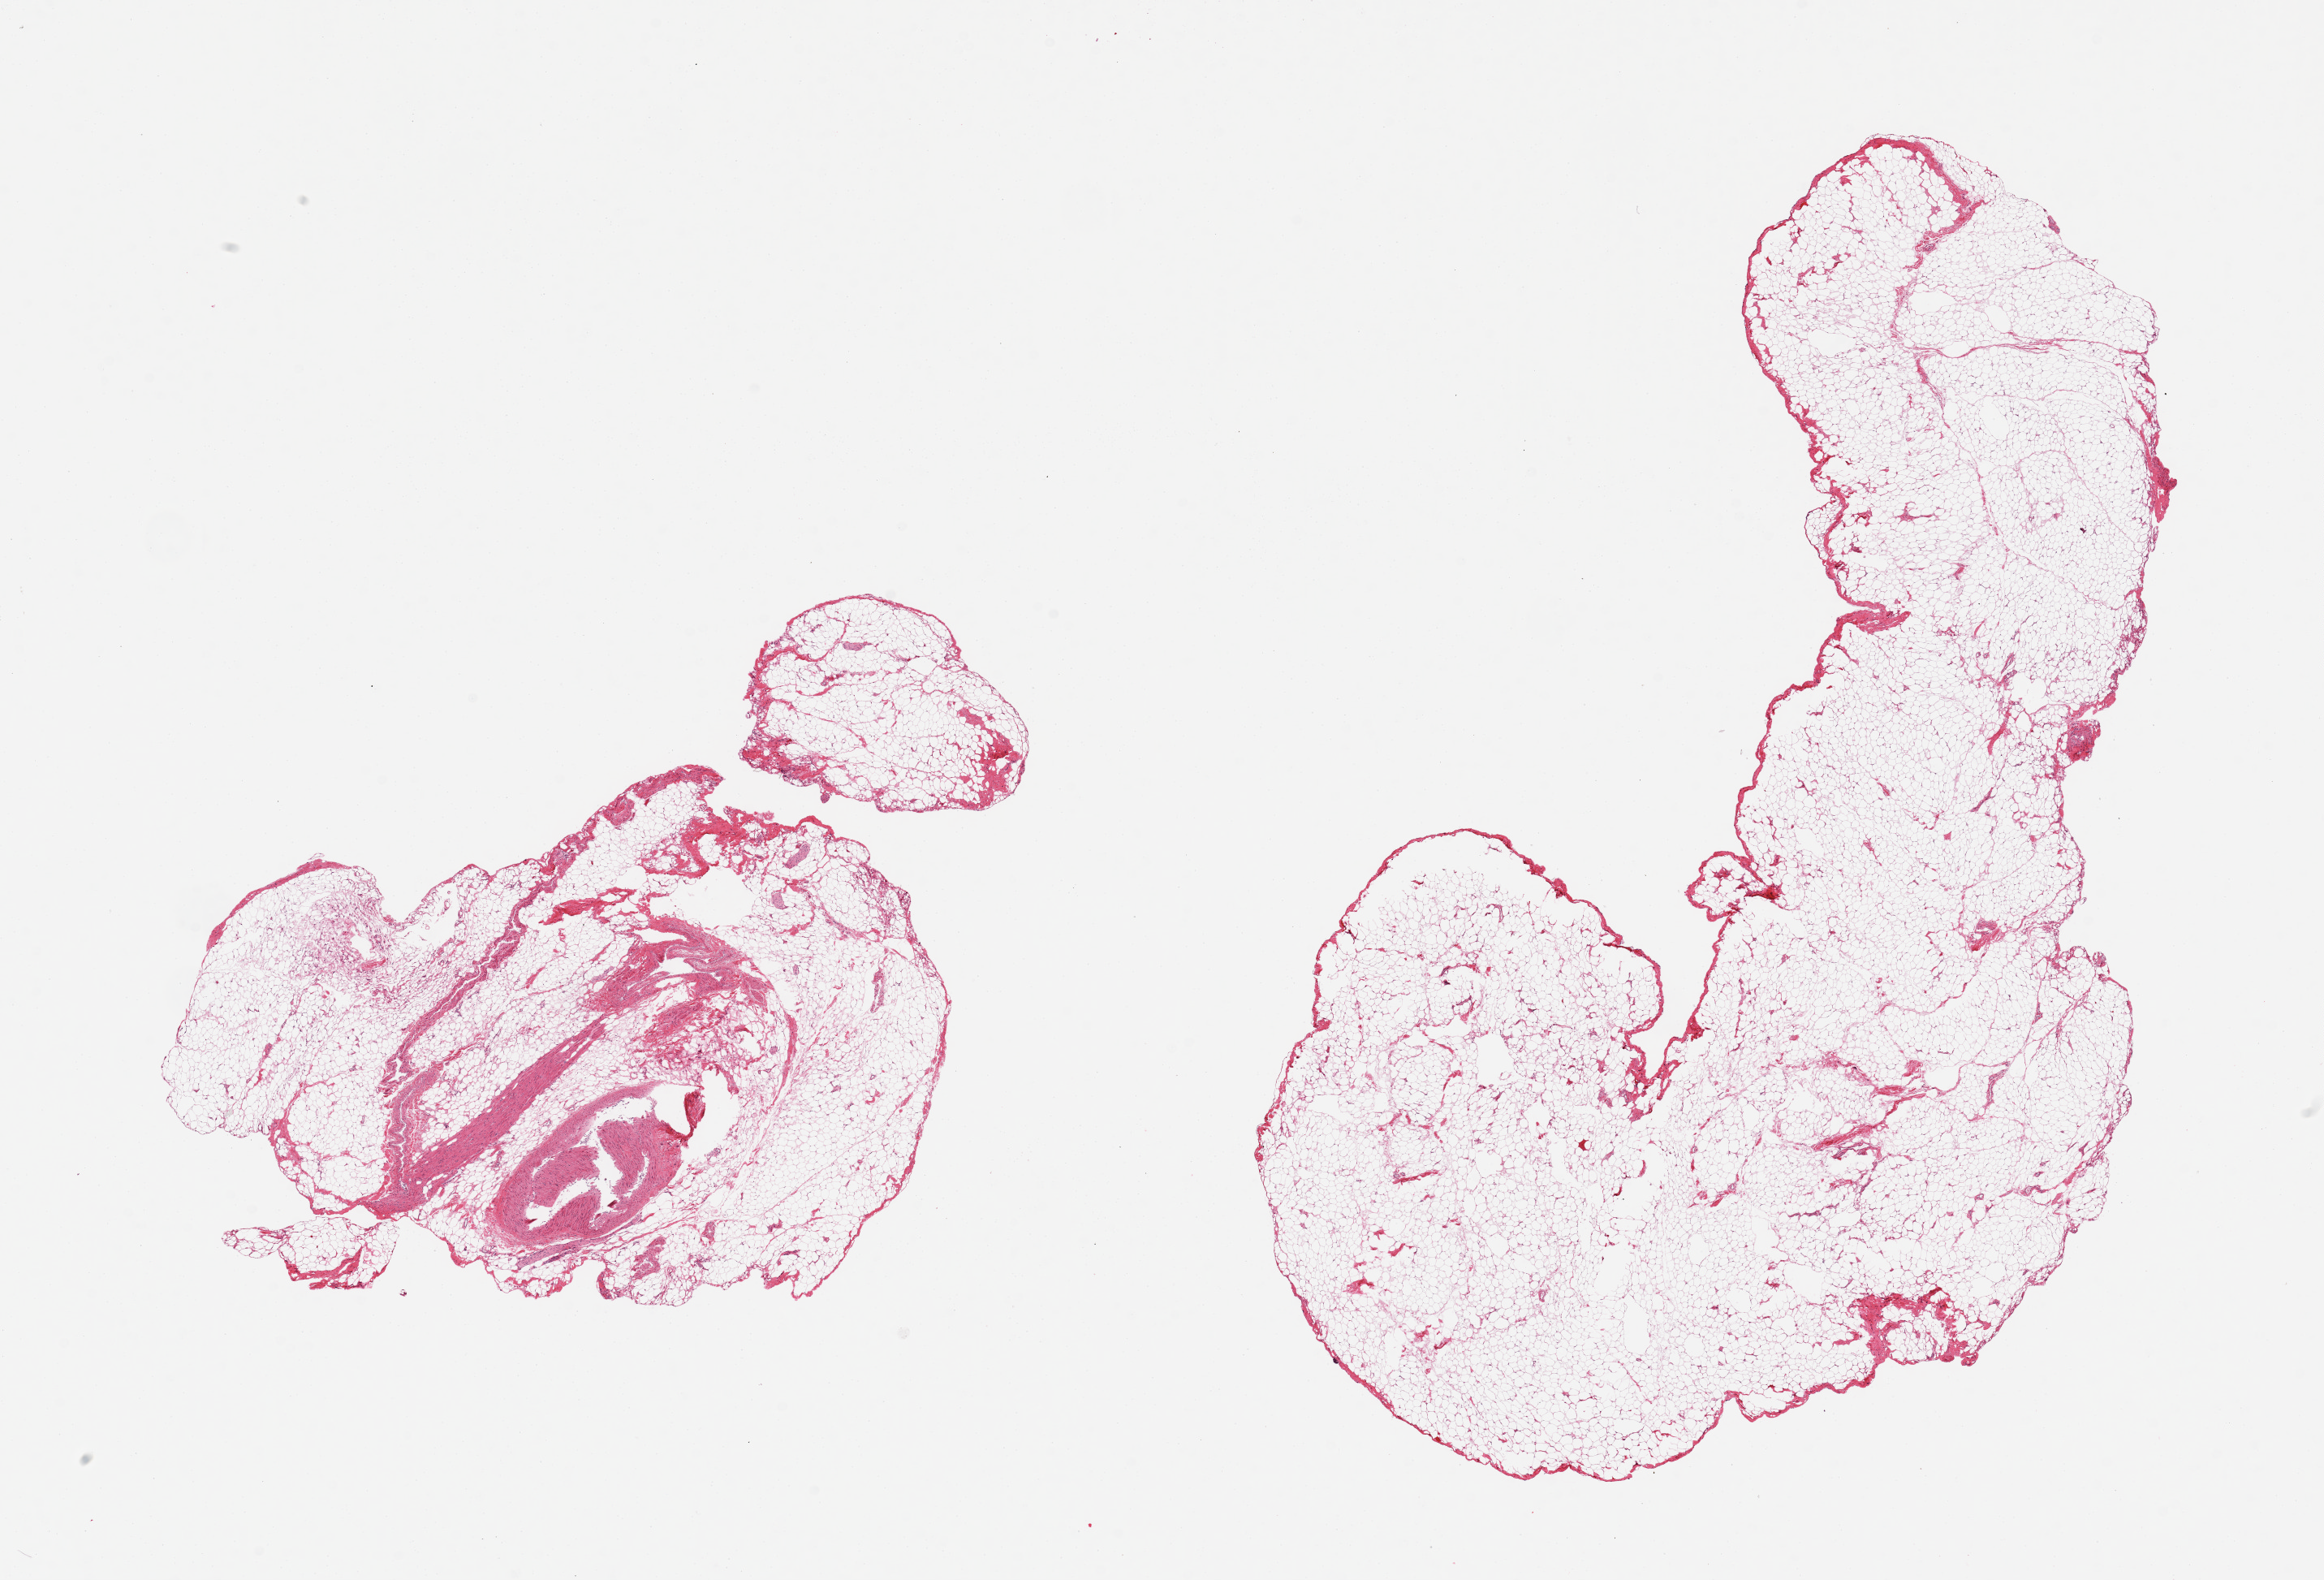
Whole-slide image, H&E stain — a low-resolution overview of the entire scanned area, about 22.6 x 15.4 mm (from a 20x scan). PAXgene-fixed, paraffin-embedded tissue. Sampled site (target tissue): omentum. Tissue donor sample. Donor sex: male.
Review note (as recorded): 2 pieces; 10% fibrovascular content in 1, 1% in other.